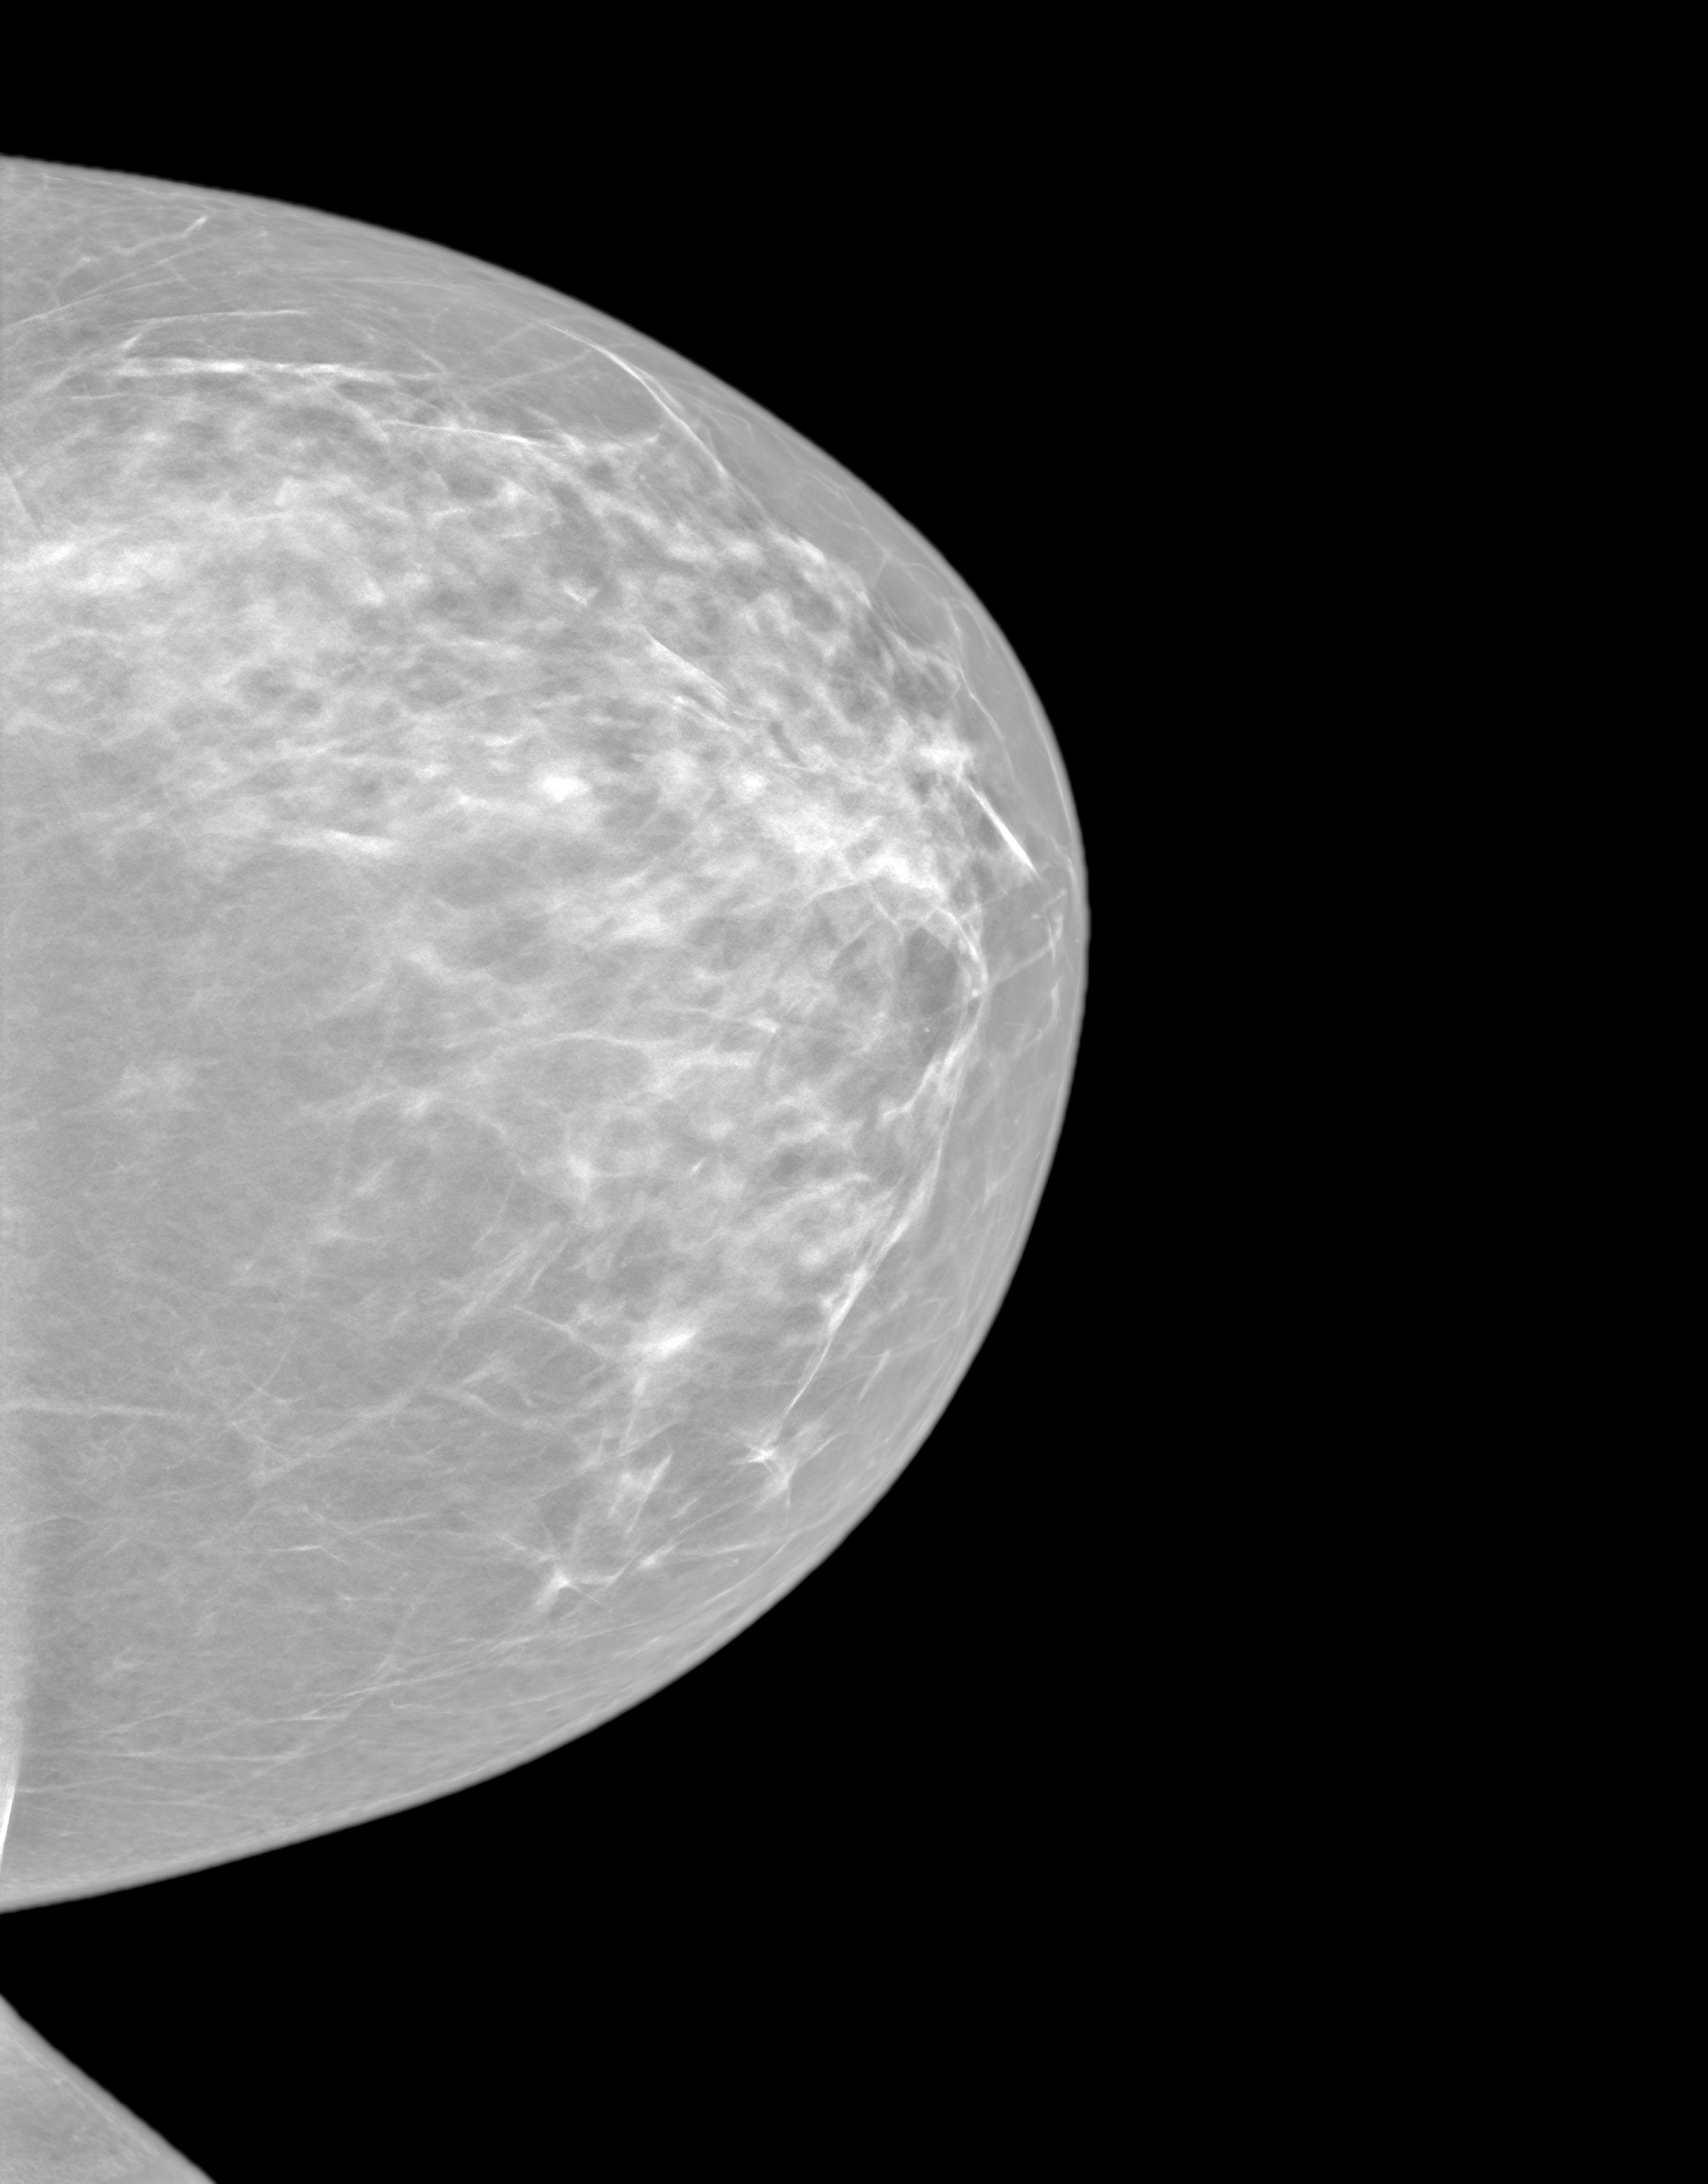
Annual screening mammography examination. Female patient, age 43 years.
Image type: synthesized 2-D view from tomosynthesis. Breast: left. Projection: CC view.